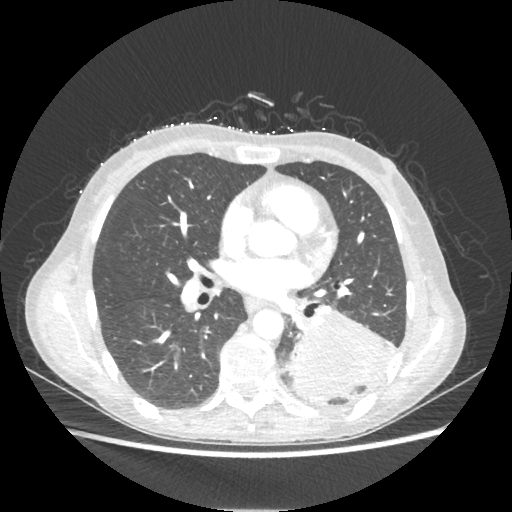
Chest CT, one axial slice; position 109 of 221 along the scan axis; reconstruction kernel STANDARD; lung window (W 1500 / L -600 HU); 1.25 mm slice thickness; 512 × 512 image matrix. Female patient, age 53 years. From the clinical record (not read from this slice): clinical TNM (as recorded): T3 N0 M0.
Structures marked on this image (rectangle marked by the reading radiologist):
- lung tumour (recorded histology: adenocarcinoma): bounding box (x1, y1, x2, y2) in pixels: (289, 311, 392, 404)